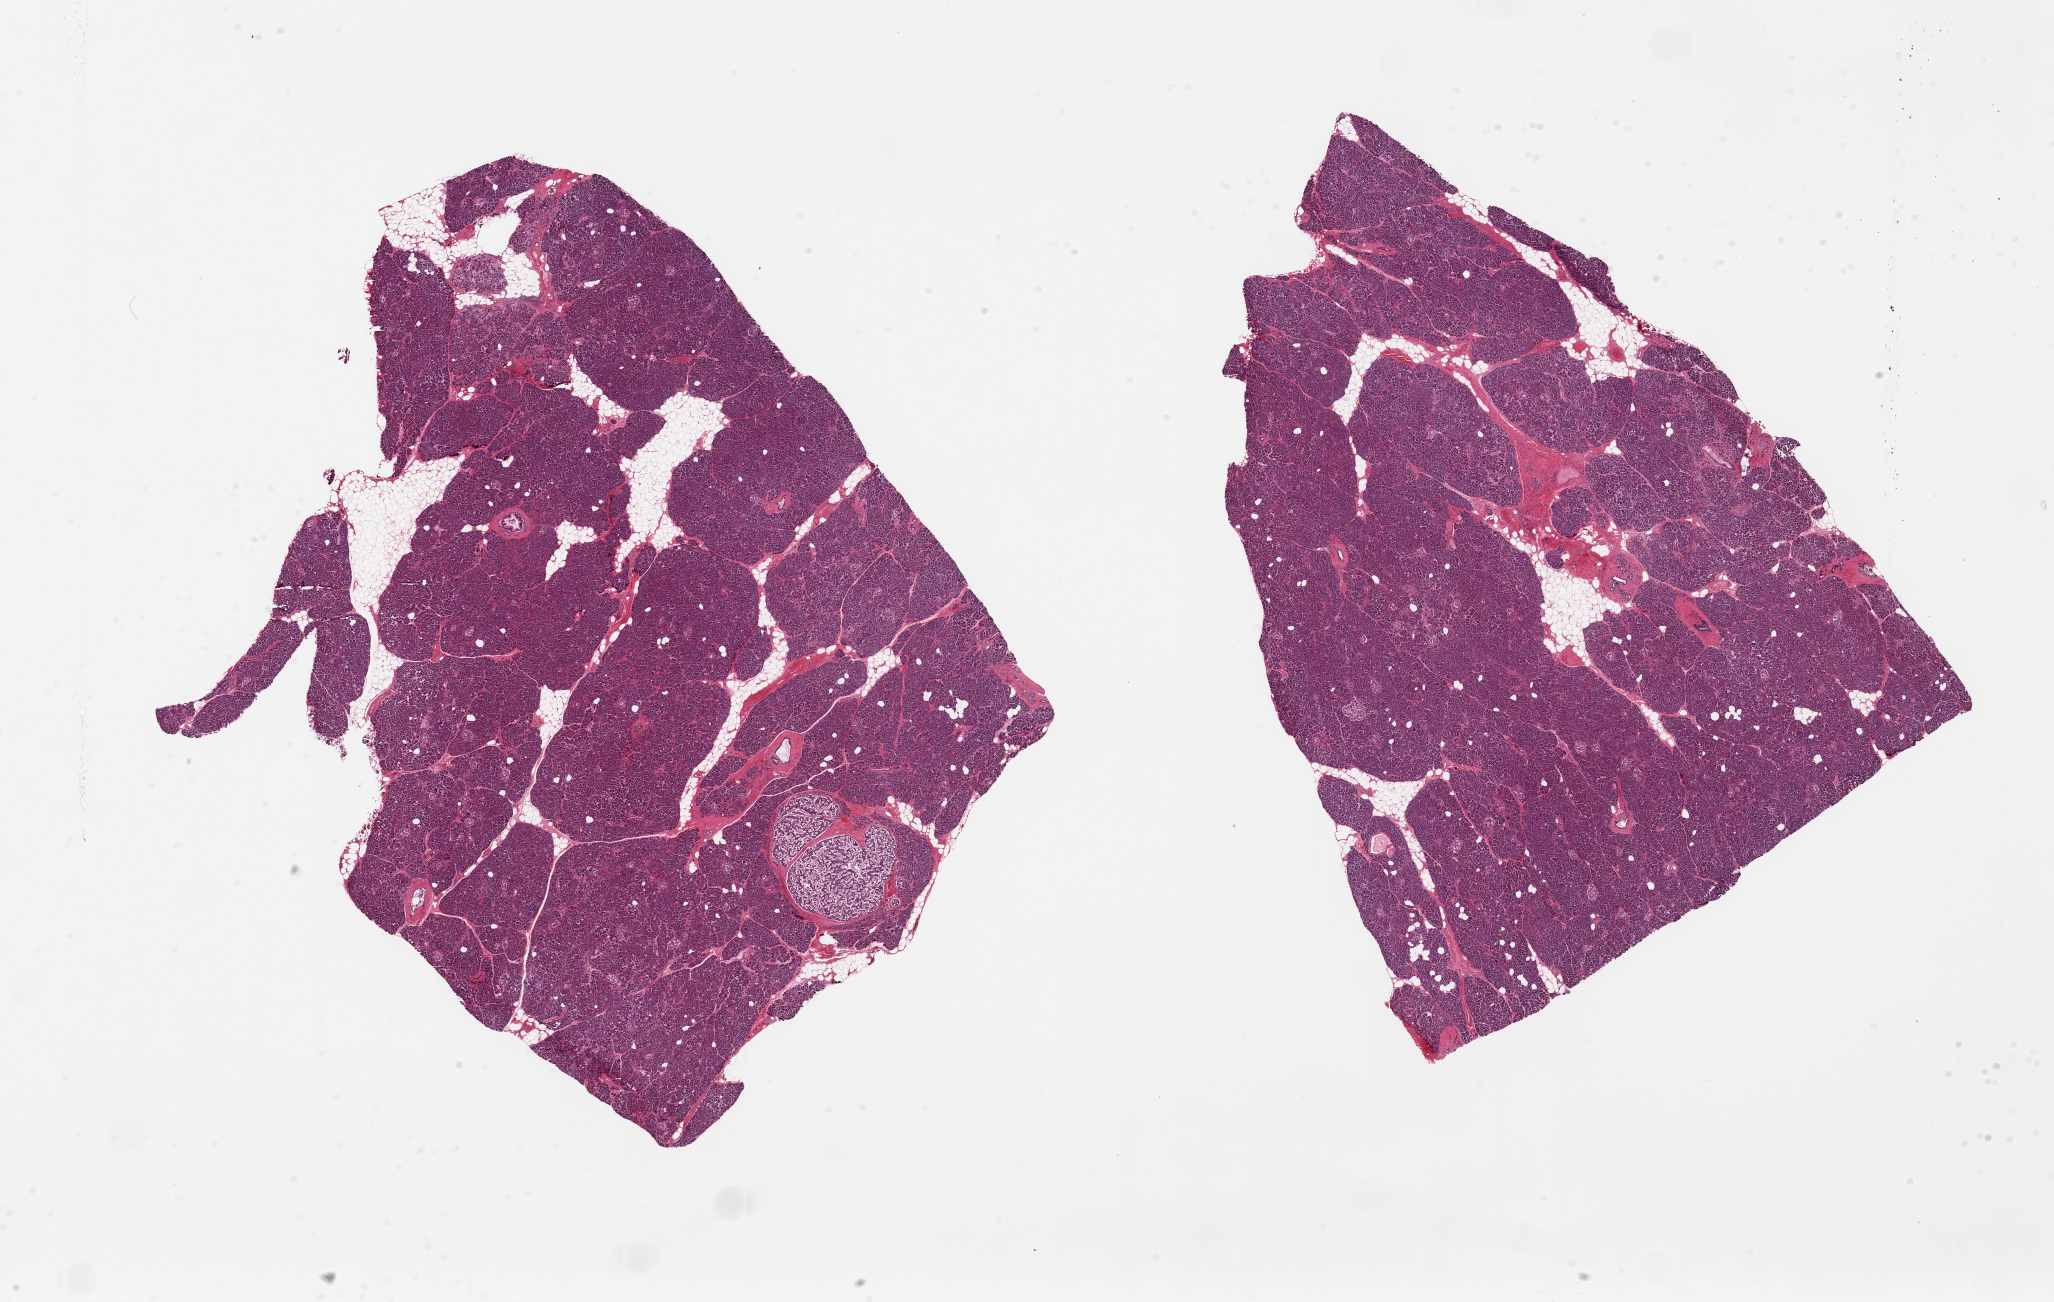
Digitized haematoxylin and eosin-stained section, a low-resolution overview of the entire scanned area, about 32.5 x 20.6 mm (from a 20x scan). PAXgene-fixed paraffin-embedded (PFPE) section. Section of pancreas (target tissue). Tissue donor sample. Donor: female.
- pathologist's review note for this sample: 2 pieces, 14x12 & 14x11mm; incidental neuroendocrine tumor ~2.5mm d (Islet cell tumor); Well visualized islets